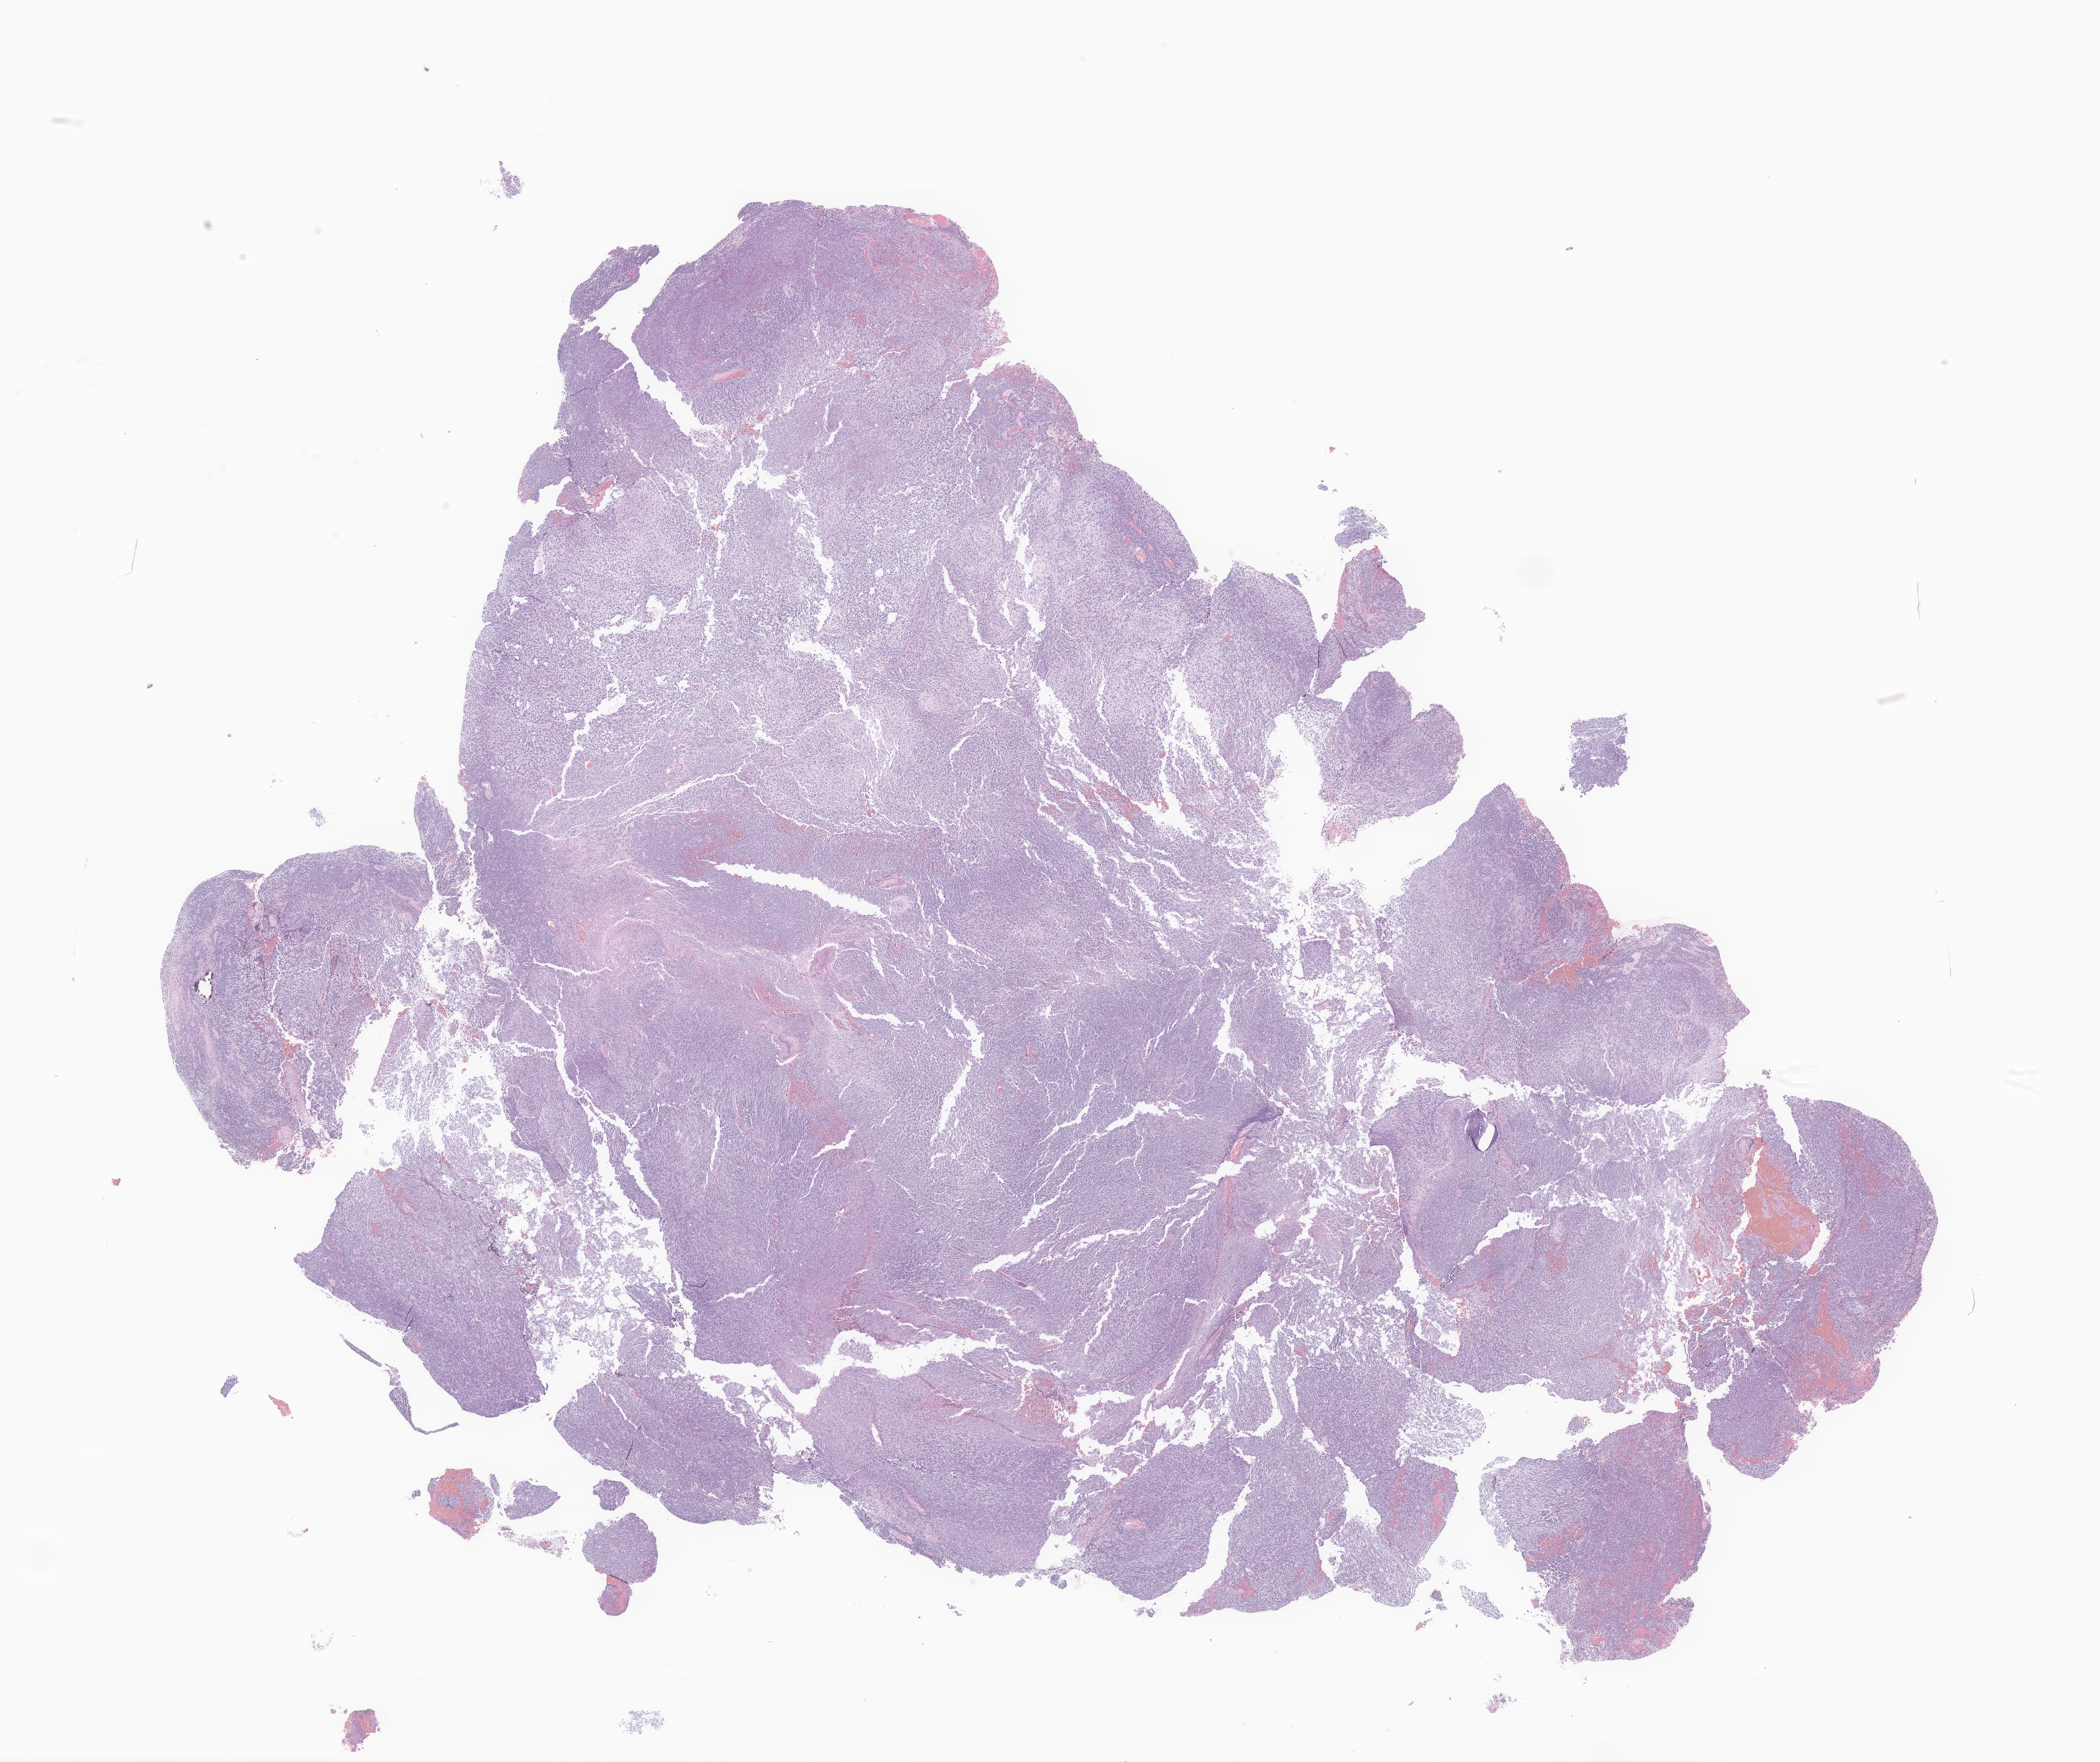
Whole-slide image, haematoxylin and eosin stain of tumor tissue from the cerebellum — whole scanned area (about 25.6 x 21.5 mm) shown as a low-resolution overview. FFPE section. Patient: male, age 113 months (9 years 5 months).
* diagnosis (ICD-O-3 morphology term): Medulloblastoma, NOS